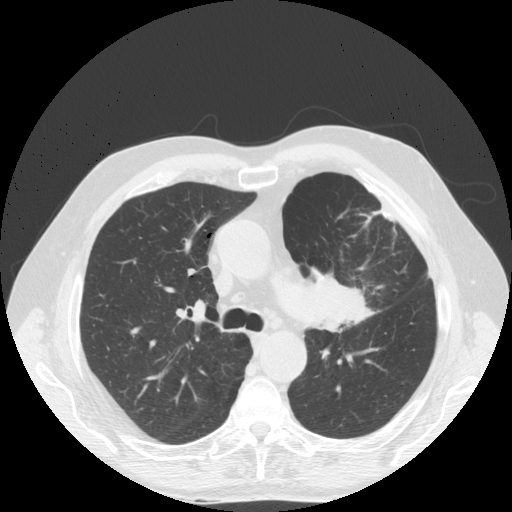
Low-dose screening chest CT, one axial slice. Position 116 of 170 along the scan axis. Reconstruction kernel STANDARD. 140 kVp. Lung window (W 1500 / L -600 HU). 2.5 mm slice thickness. 512 × 512 image matrix.
Outlined on this slice (manually delineated by an expert):
- lesion 1 (tumor, upper lobe of left lung): bounding box [x1, y1, x2, y2] px = [306, 267, 376, 333]